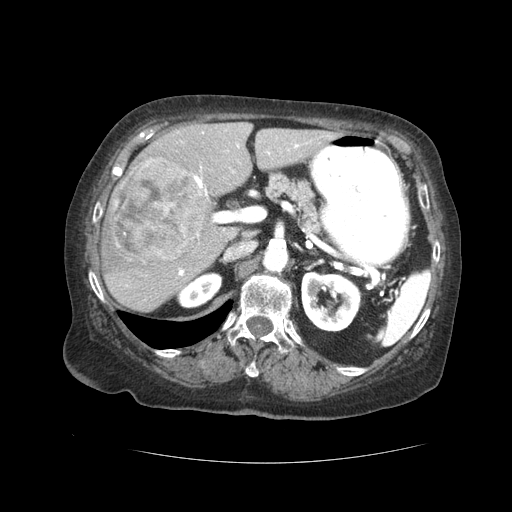
Contrast-enhanced abdominal CT (liver protocol), one axial slice; soft-tissue window (W 400 / L 40 HU); 2.5 mm slice thickness; 512 × 512 image matrix. Case-level facts recorded for this patient, not image findings: diagnosis: hepatocellular carcinoma (patient treated with transarterial chemoembolisation; whether this scan precedes or follows treatment is not stated here); TNM stage (as recorded): Stage-I; Child-Pugh class: A; tumour nodularity: uninodular.
Annotated regions visible in this slice (semi-automatic segmentation, software-assisted and operator-edited):
- liver parenchyma outside the tumour (the mass and vessels are separate outlines, so this box may not span the whole liver): bounding box [x1, y1, x2, y2] px = [102, 122, 337, 312]
- mass: [107, 157, 206, 261]
- liver vessels: [126, 136, 330, 286]